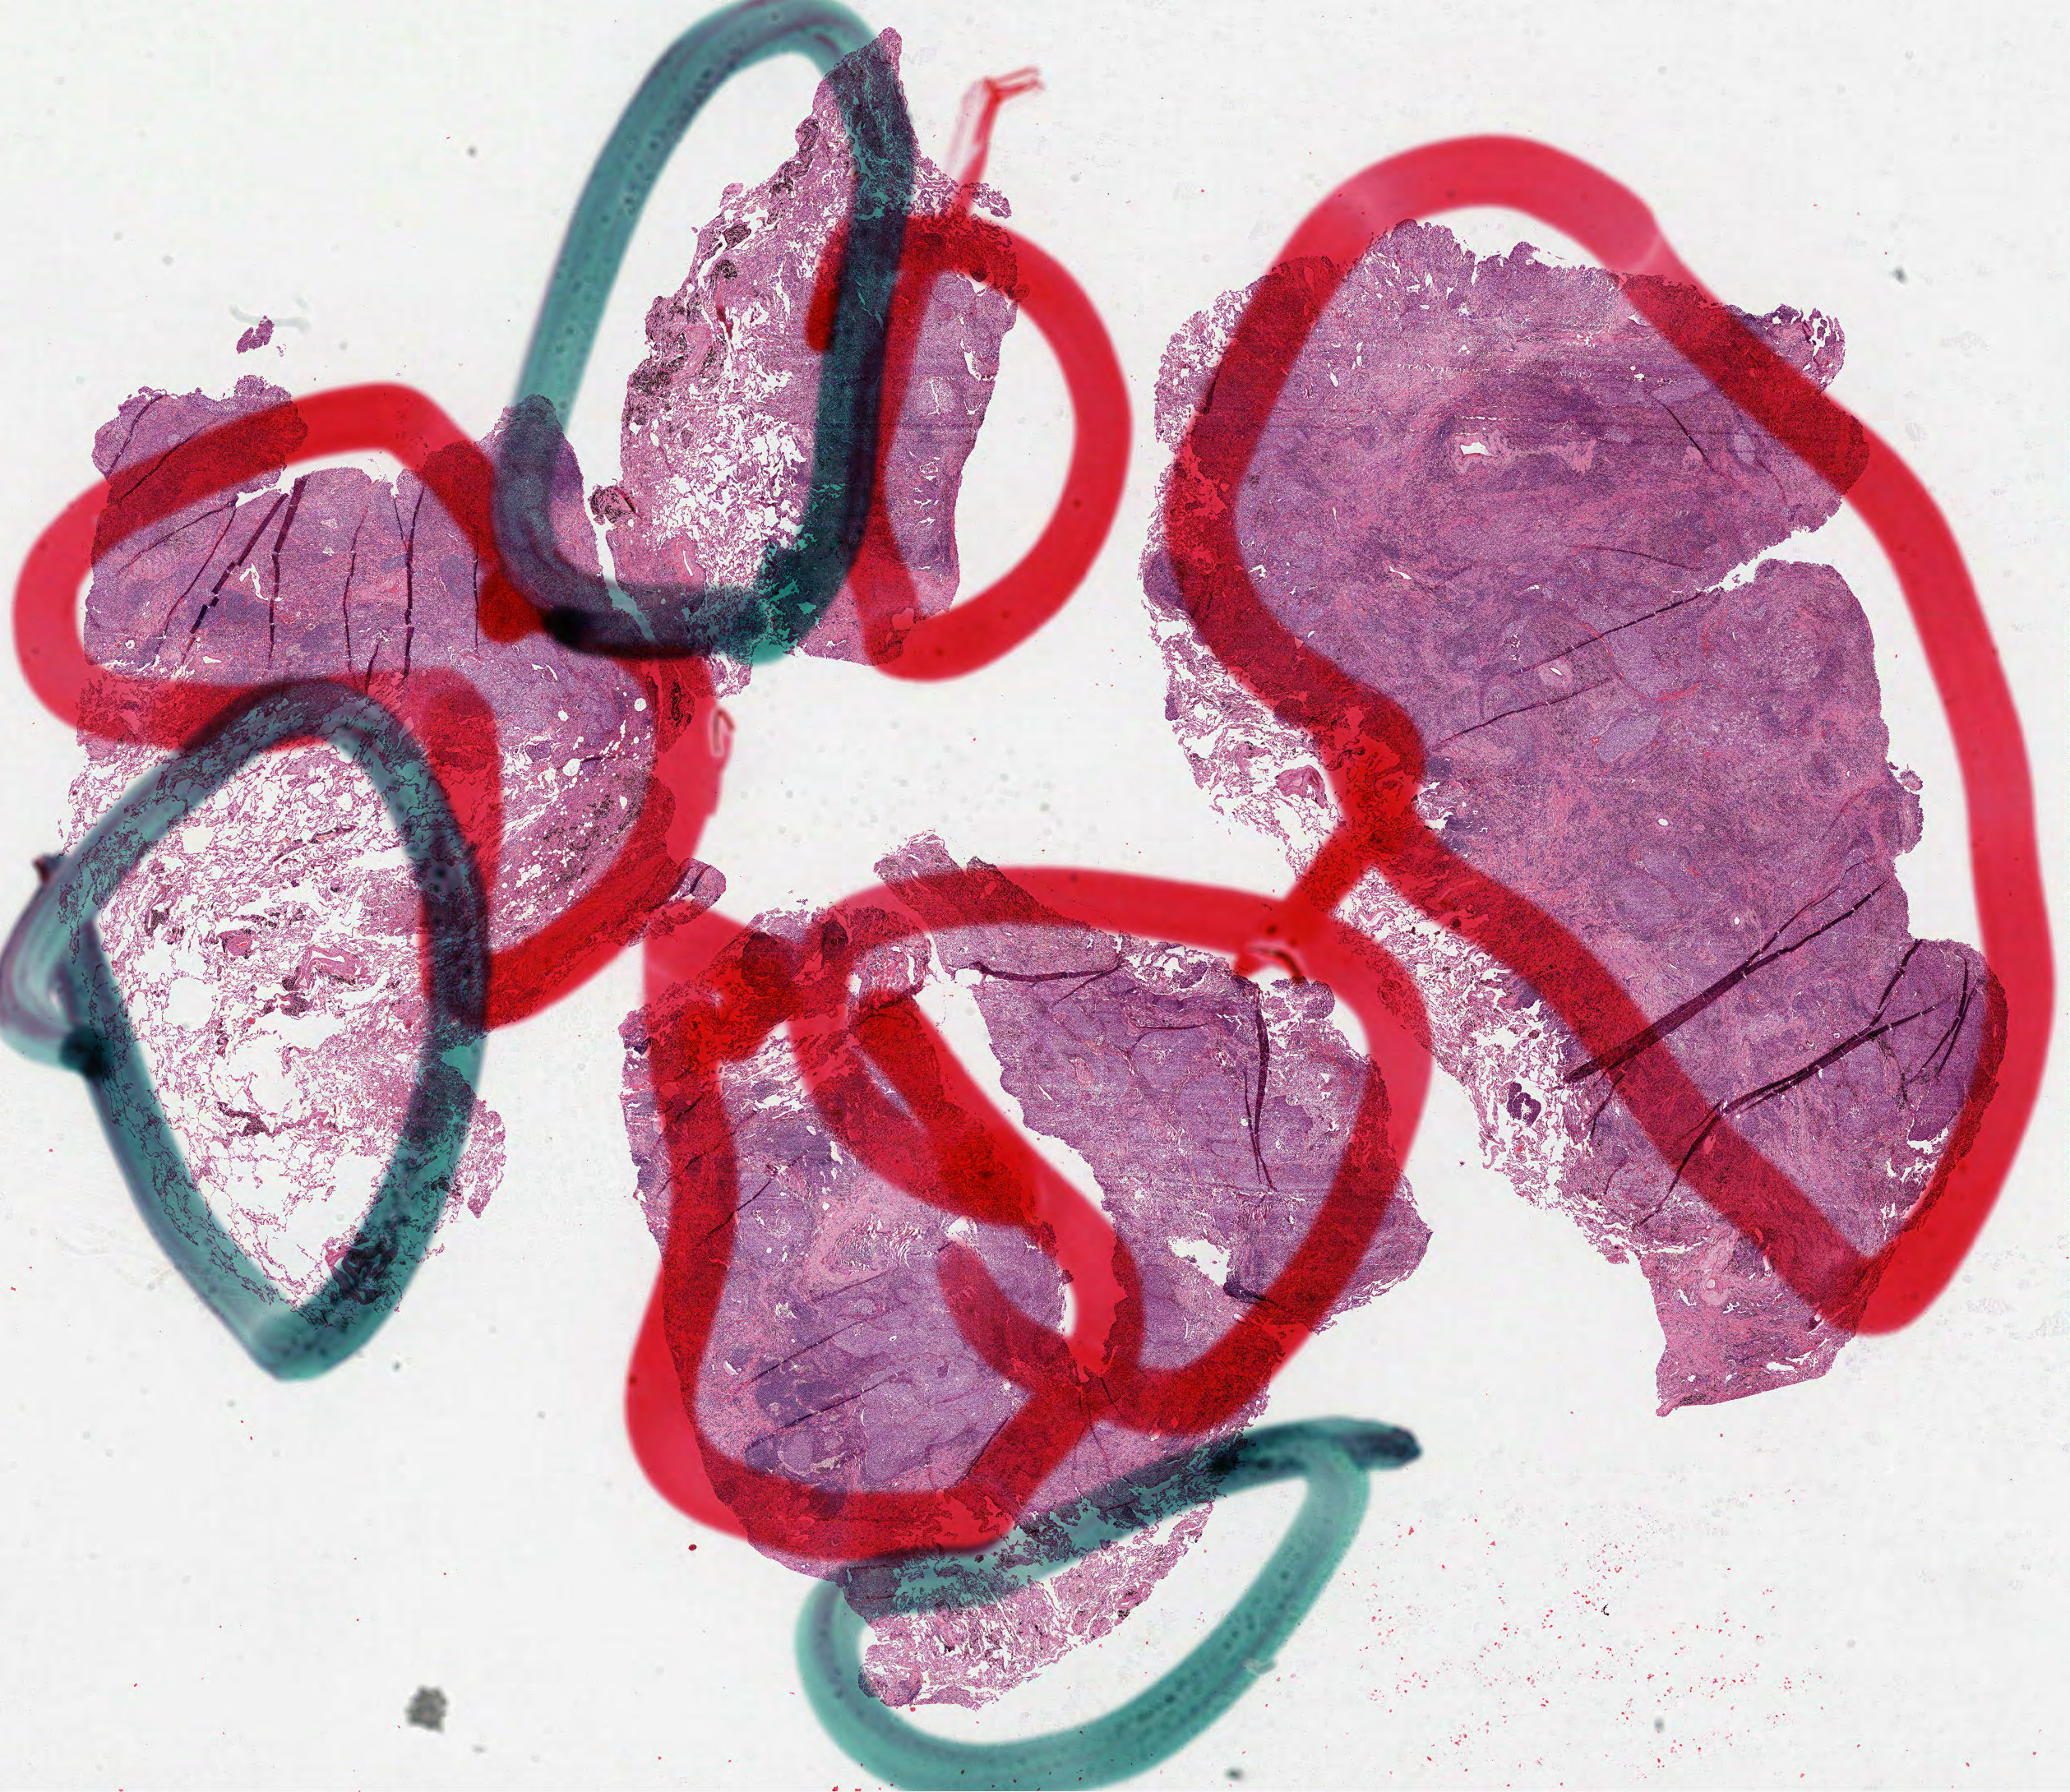
Hematoxylin and eosin (H&E) stained whole-slide image — low-resolution overview of the scanned area, about 20.3 x 17.6 mm, formalin-fixed paraffin-embedded (FFPE) diagnostic section, primary tumour sample from the lung. Patient: male, age at initial diagnosis 60 years.
Laterality: left. Histologic diagnosis: Squamous cell carcinoma, NOS. AJCC pathologic stage: IA (7th edition).